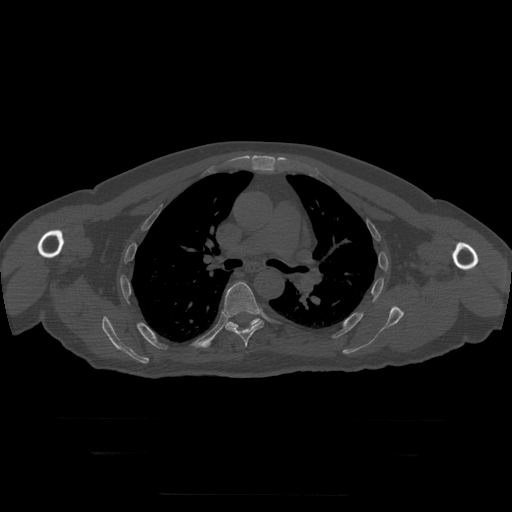
CT including the spine, one axial slice; position 202 of 397 along the scan axis; reconstruction kernel STANDARD; 120 kVp; bone window (W 1800 / L 400 HU); 1.25 mm slice thickness; 512 × 512 image matrix. Patient age 73 years. Case-level facts recorded for this patient, not image findings: primary cancer: prostate.
Structures marked on this image (semi-automatic segmentation, software-assisted and operator-edited):
- T6 vertebra: bounding box [x1, y1, x2, y2] px = [224, 282, 264, 348]
- T7 vertebra: [227, 319, 261, 328]